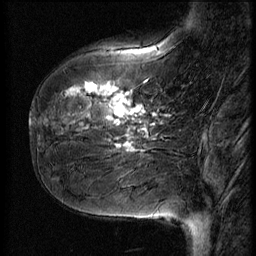
Breast MRI (dynamic contrast-enhanced), one sagittal slice. Slice 17 of 56 in the series (ordered by position). 3 images stored at this slice position (order not interpretable as contrast timing). 1.5 T. TE 4.2 ms, TR 9 ms. 2.5 mm slice thickness. 256 × 256 image matrix. Patient: female, 51 years. From the clinical record (not read from this slice): setting: breast cancer imaged before/during neoadjuvant chemotherapy; receptor status: HR-positive, HER2-negative.
Structures marked on this image (semi-automatic segmentation, software-assisted and operator-edited):
- analysis volume of interest (the breast-tissue region the enhancement analysis was run in; not a lesion): box from (x=41, y=58) to (x=167, y=161) px
- tumour enhancement mask (voxels above the 140 % enhancement threshold inside the analysis volume of interest): (x=67, y=83)–(x=155, y=153)